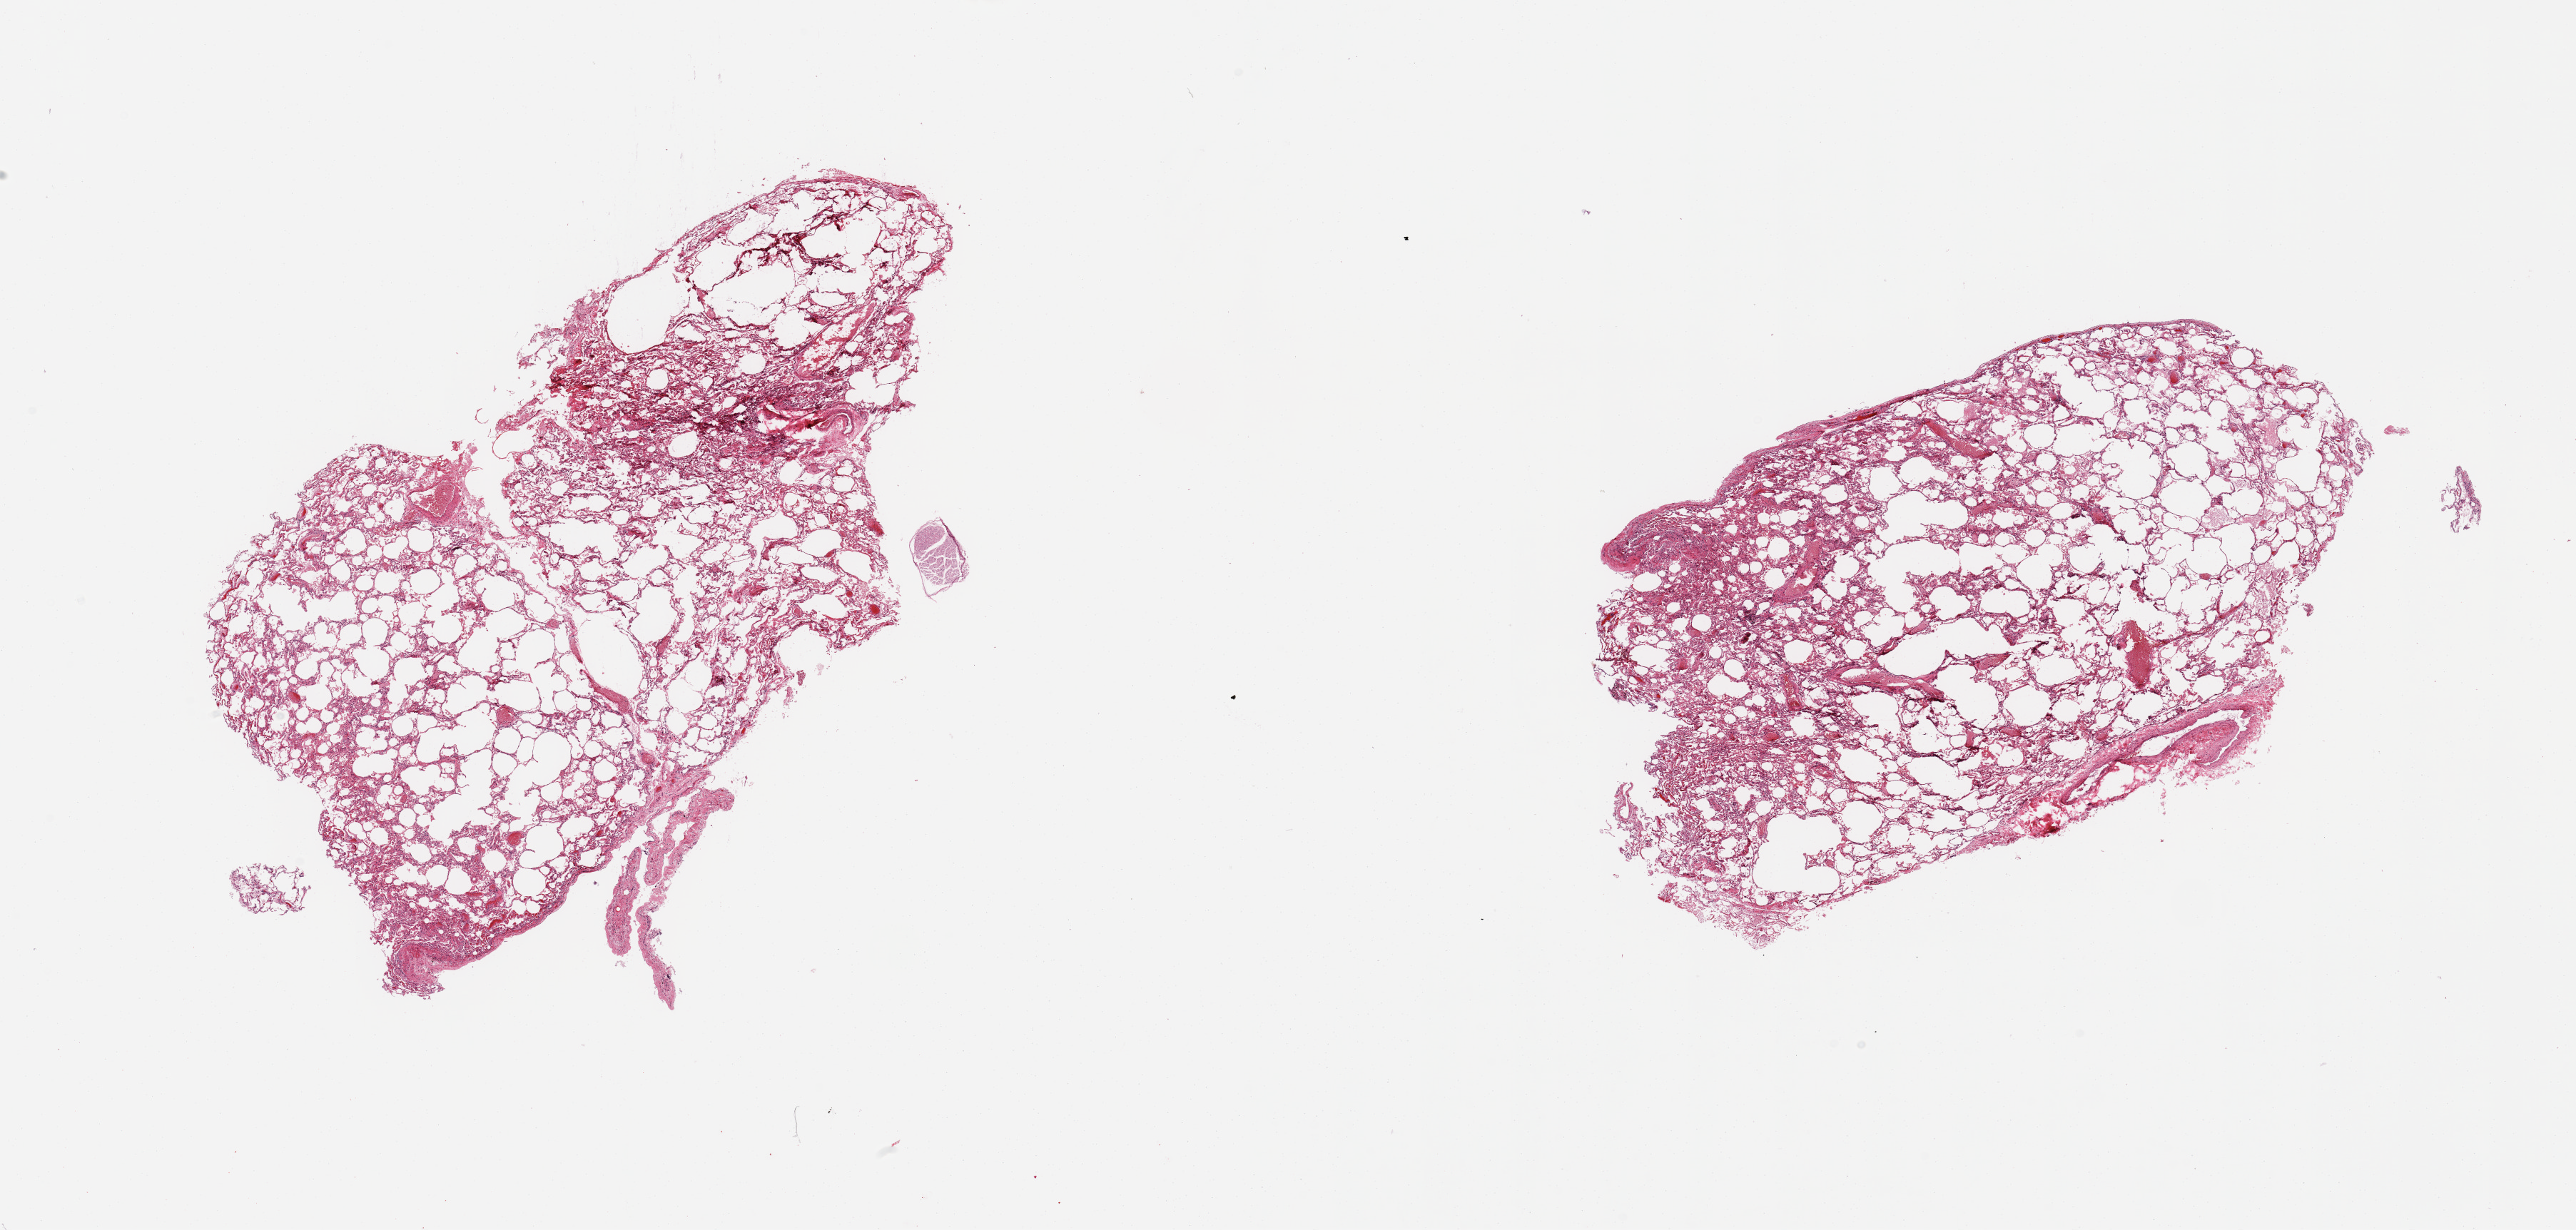
Haematoxylin and eosin whole-slide image, brightfield — whole scanned area (about 28.5 x 13.6 mm) shown as a low-resolution overview; PAXgene-fixed, paraffin-embedded tissue; target tissue: lung; donor tissue sample. Donor sex: female.
Reviewer comment on this tissue sample: 2 pieces, emphysematous changes.